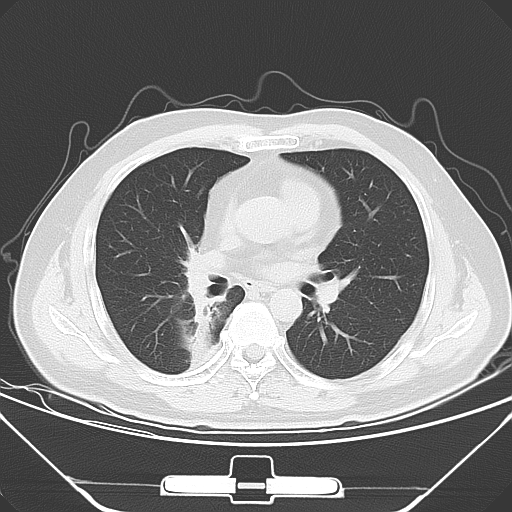
Chest CT, one axial slice. Slice 29 of 56 in the series (ordered by position). 120 kVp. Lung window (W 1500 / L -600 HU). 5 mm slice thickness. 512 × 512 image matrix, field of view 371 × 371 mm. Patient: male, 48 years. From the clinical record (not read from this slice): clinical TNM (as recorded): T1a N1 M1c; histopathological grade: G3.
Annotated regions visible in this slice (bounding box drawn by a radiologist):
- lung tumour (recorded histology: adenocarcinoma): bounding box [x1, y1, x2, y2] px = [175, 249, 217, 350]